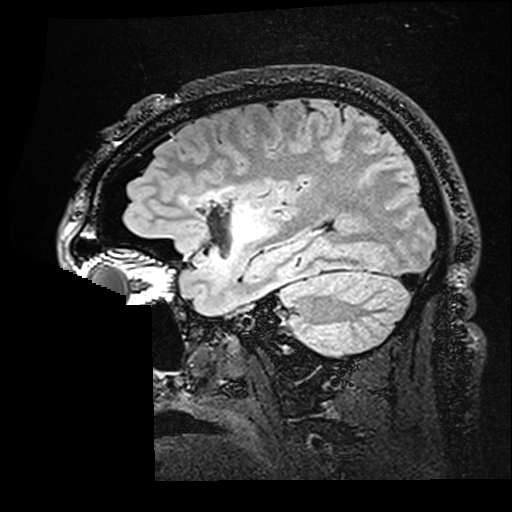
Brain MRI from a brain-tumour surgery series, one sagittal slice; slice 121 of 176 in the series (ordered by position); T2 FLAIR; 512 × 512 image matrix, field of view 250 × 250 mm. Case-level facts recorded for this patient, not image findings: histopathology: Astrocytoma; WHO grade: 2; IDH mutation: yes; tumour location: Right Insular.
Annotated regions visible in this slice (expert manual segmentation):
- residual tumour: box from (x=183, y=187) to (x=267, y=246) px